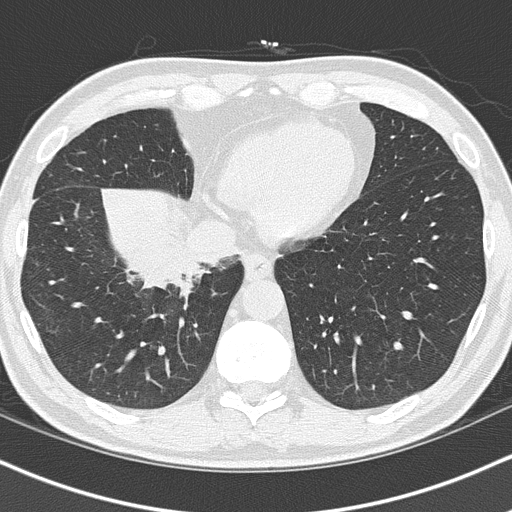
Low-dose screening chest CT, one axial slice; position 33 of 151 along the scan axis; reconstruction kernel B50f; lung window (W 1500 / L -600 HU); 2 mm slice thickness; 512 × 512 image matrix, field of view 320 × 320 mm.
Structures marked on this image (outlined manually by an expert reader):
- lesion 1 (tumor, hilum of right lung): box from (x=144, y=242) to (x=199, y=284) px